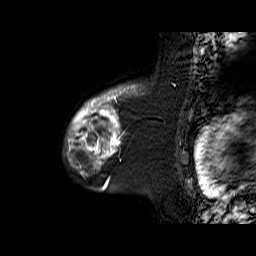
Breast MRI (dynamic contrast-enhanced), one sagittal slice; slice 51 of 60 in the series (ordered by position); dynamic contrast-enhanced series, time point 2 of 6 at this slice position (early post-contrast); 1.5 T; TE 6.3 ms, TR 32.9 ms; 4 mm slice thickness; 256 × 256 image matrix, field of view 200 × 200 mm. Female patient. Case-level facts recorded for this patient, not image findings: setting: breast cancer imaged before/during neoadjuvant chemotherapy; receptor status: triple-negative.
Outlined on this slice (semi-automatic segmentation, software-assisted and operator-edited):
- analysis volume of interest (the breast-tissue region the enhancement analysis was run in; not a lesion): bounding box [x1, y1, x2, y2] px = [65, 86, 145, 170]
- tumour enhancement mask (voxels above the 100 % enhancement threshold inside the analysis volume of interest): [67, 86, 131, 170]